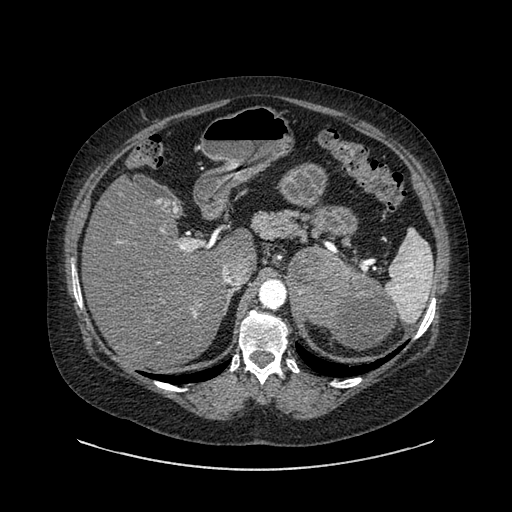
Contrast-enhanced abdominal CT, one axial slice. Position 599 of 769 along the scan axis. Reconstruction kernel SOFT. 120 kVp. Intravenous contrast given. Soft-tissue window (W 400 / L 40 HU). 0.62 mm slice thickness. 512 × 512 image matrix, field of view 460 × 460 mm. Female patient, age 61 years. From the clinical record (not read from this slice): diagnosis: adrenocortical carcinoma; tumour side: left adrenal; tumour size at pathology: 13 cm; Ki-67 index: 79 %; stage (as recorded): 2.
Structures marked on this image (semi-automatically segmented with operator editing):
- mass: bounding box (x1, y1, x2, y2) in pixels: (287, 248, 397, 350)